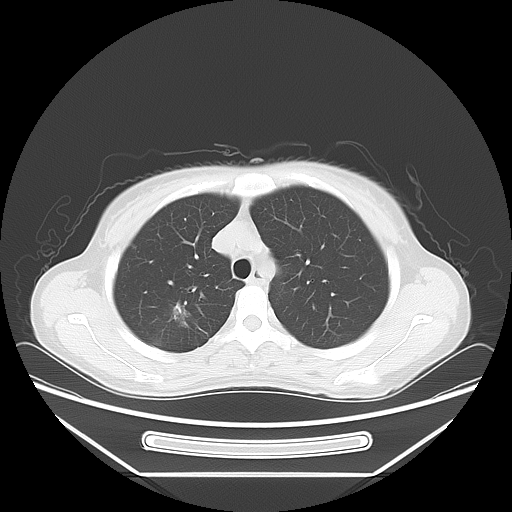
Chest CT, one axial slice; reconstruction kernel LUNG; lung window (W 1500 / L -600 HU); 5 mm slice thickness; 512 × 512 image matrix, field of view 408 × 408 mm. Female patient, age 37 years. Case-level facts recorded for this patient, not image findings: clinical TNM (as recorded): T1c N0 M1.
Annotated regions visible in this slice (bounding box drawn by a radiologist):
- lung tumour (recorded histology: adenocarcinoma): box from (x=165, y=296) to (x=194, y=330) px